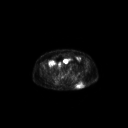
FDG PET of an extremity soft-tissue mass (from a PET/CT study), one axial slice. Position 77 of 267 along the scan axis. 3.27 mm slice thickness. 128 × 128 image matrix. Male patient, age 69 years. Case-level facts recorded for this patient, not image findings: histological type: leiomyosarcoma; grade: intermediate; site of the primary tumour: left pelvis.
Outlined on this slice (expert contour drawn on MRI and transferred to this co-registered scan by the dataset authors):
- gross tumour volume (mass): bounding box (x1, y1, x2, y2) in pixels: (75, 81, 84, 89)